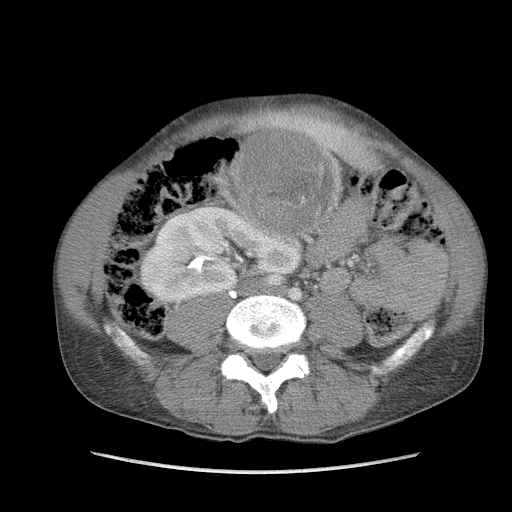
Contrast-enhanced abdominal CT, one axial slice. Slice 40 of 115 in the series (ordered by position). Soft-tissue window (W 400 / L 40 HU). 5 mm slice thickness. 512 × 512 image matrix. Male patient. From the clinical record (not read from this slice): diagnosis: adrenocortical carcinoma; tumour side: right adrenal; Ki-67 index: 13 %; stage (as recorded): 3.
Structures marked on this image (semi-automatic segmentation, software-assisted and operator-edited):
- mass: bounding box (x1, y1, x2, y2) in pixels: (237, 131, 332, 231)